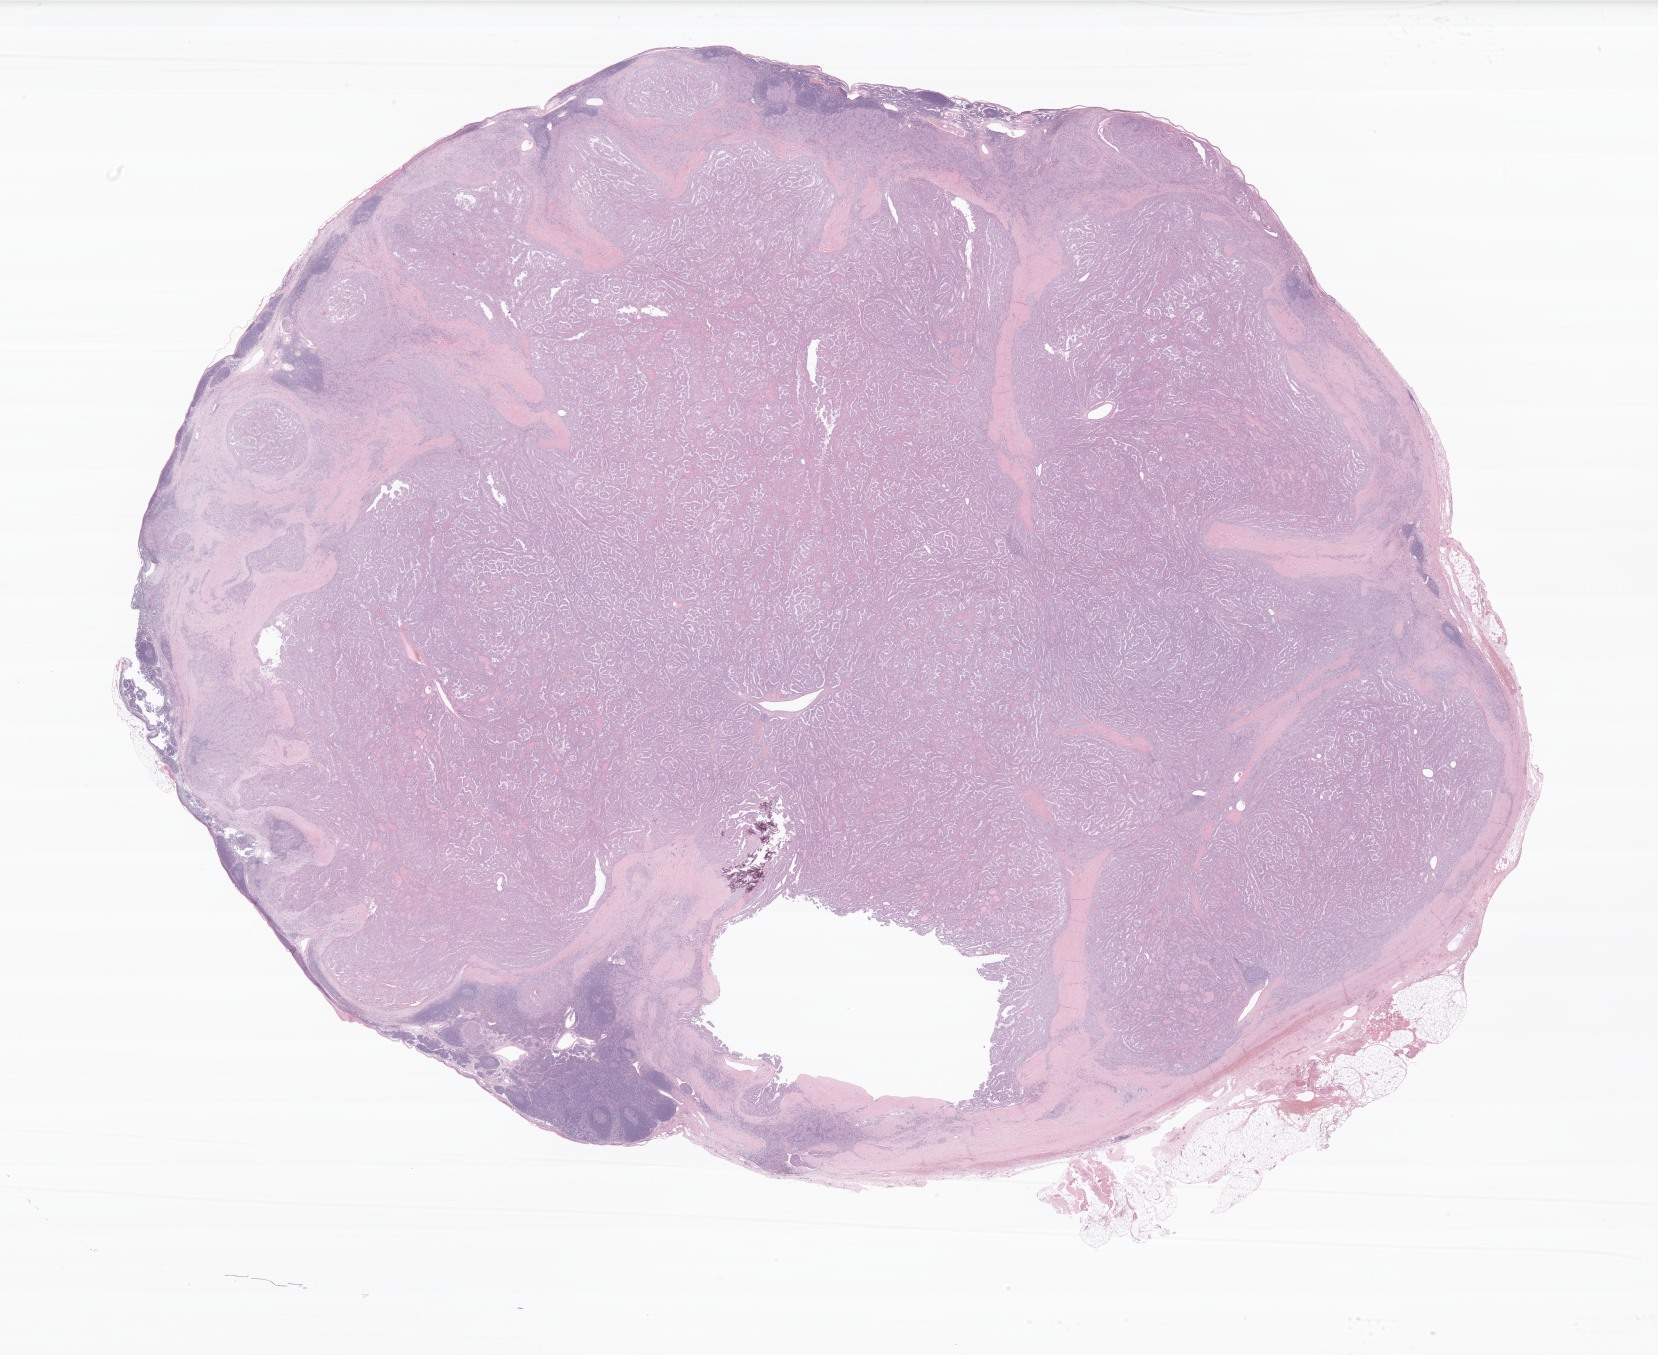
Whole-slide image, hematoxylin and eosin (H&E) stain of tumor tissue from the thyroid — low-resolution overview of the scanned area, about 27.9 x 22.8 mm; formalin-fixed, paraffin-embedded (FFPE) tissue. Female patient, age 160 months (13 years 4 months).
- recorded diagnosis: Papillary carcinoma, NOS